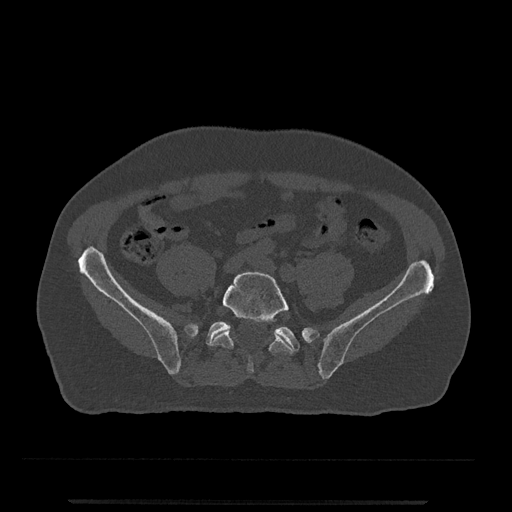
CT including the spine, one axial slice; position 55 of 797 along the scan axis; 120 kVp; bone window (W 1800 / L 400 HU); 512 × 512 image matrix, field of view 419 × 419 mm. Male patient, age 63 years. Case-level facts recorded for this patient, not image findings: primary cancer: prostate.
Structures marked on this image (semi-automatic segmentation, software-assisted and operator-edited):
- L5 vertebra: bounding box [x1, y1, x2, y2] px = [210, 271, 293, 373]